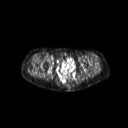
FDG PET of an extremity soft-tissue mass (from a PET/CT study), one axial slice; slice 54 of 267 in the series (ordered by position); 128 × 128 image matrix, field of view 600 × 600 mm. Female patient, age 57 years. From the clinical record (not read from this slice): histological type: epithelioid sarcoma with vascular differentiation; site of the primary tumour: right buttock.
Annotated regions visible in this slice (expert contour drawn on MRI and transferred to this co-registered scan by the dataset authors):
- gross tumour volume (mass): box from (x=26, y=66) to (x=39, y=78) px